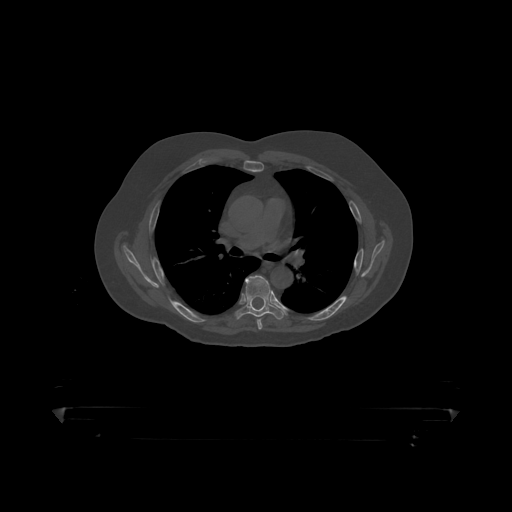
CT including the spine, one axial slice; position 305 of 390 along the scan axis; bone window (W 1800 / L 400 HU); 1.25 mm slice thickness; 512 × 512 image matrix, field of view 650 × 650 mm. Patient: male, 60 years. Case-level facts recorded for this patient, not image findings: primary cancer: prostate.
Structures marked on this image (semi-automatic segmentation, software-assisted and operator-edited):
- T6 vertebra: bounding box (x1, y1, x2, y2) in pixels: (236, 276, 283, 319)